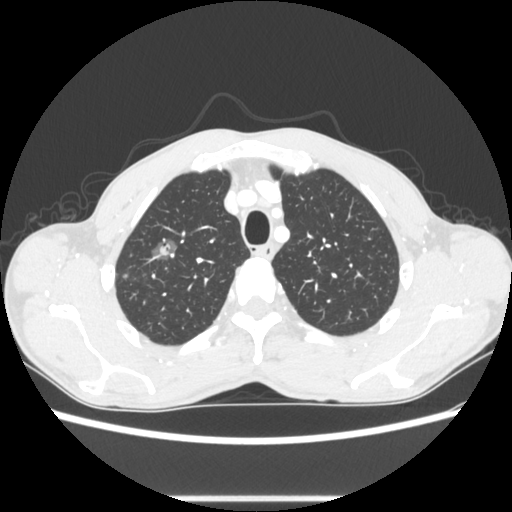
Chest CT, one axial slice; reconstruction kernel STANDARD; lung window (W 1500 / L -600 HU); 1.25 mm slice thickness; 512 × 512 image matrix. Male patient, age 54 years. From the clinical record (not read from this slice): clinical TNM (as recorded): T1a N0 M0.
Outlined on this slice (rectangle marked by the reading radiologist):
- lung tumour (recorded histology: adenocarcinoma): bounding box <146,233,181,263> (left, top, right, bottom; pixels)